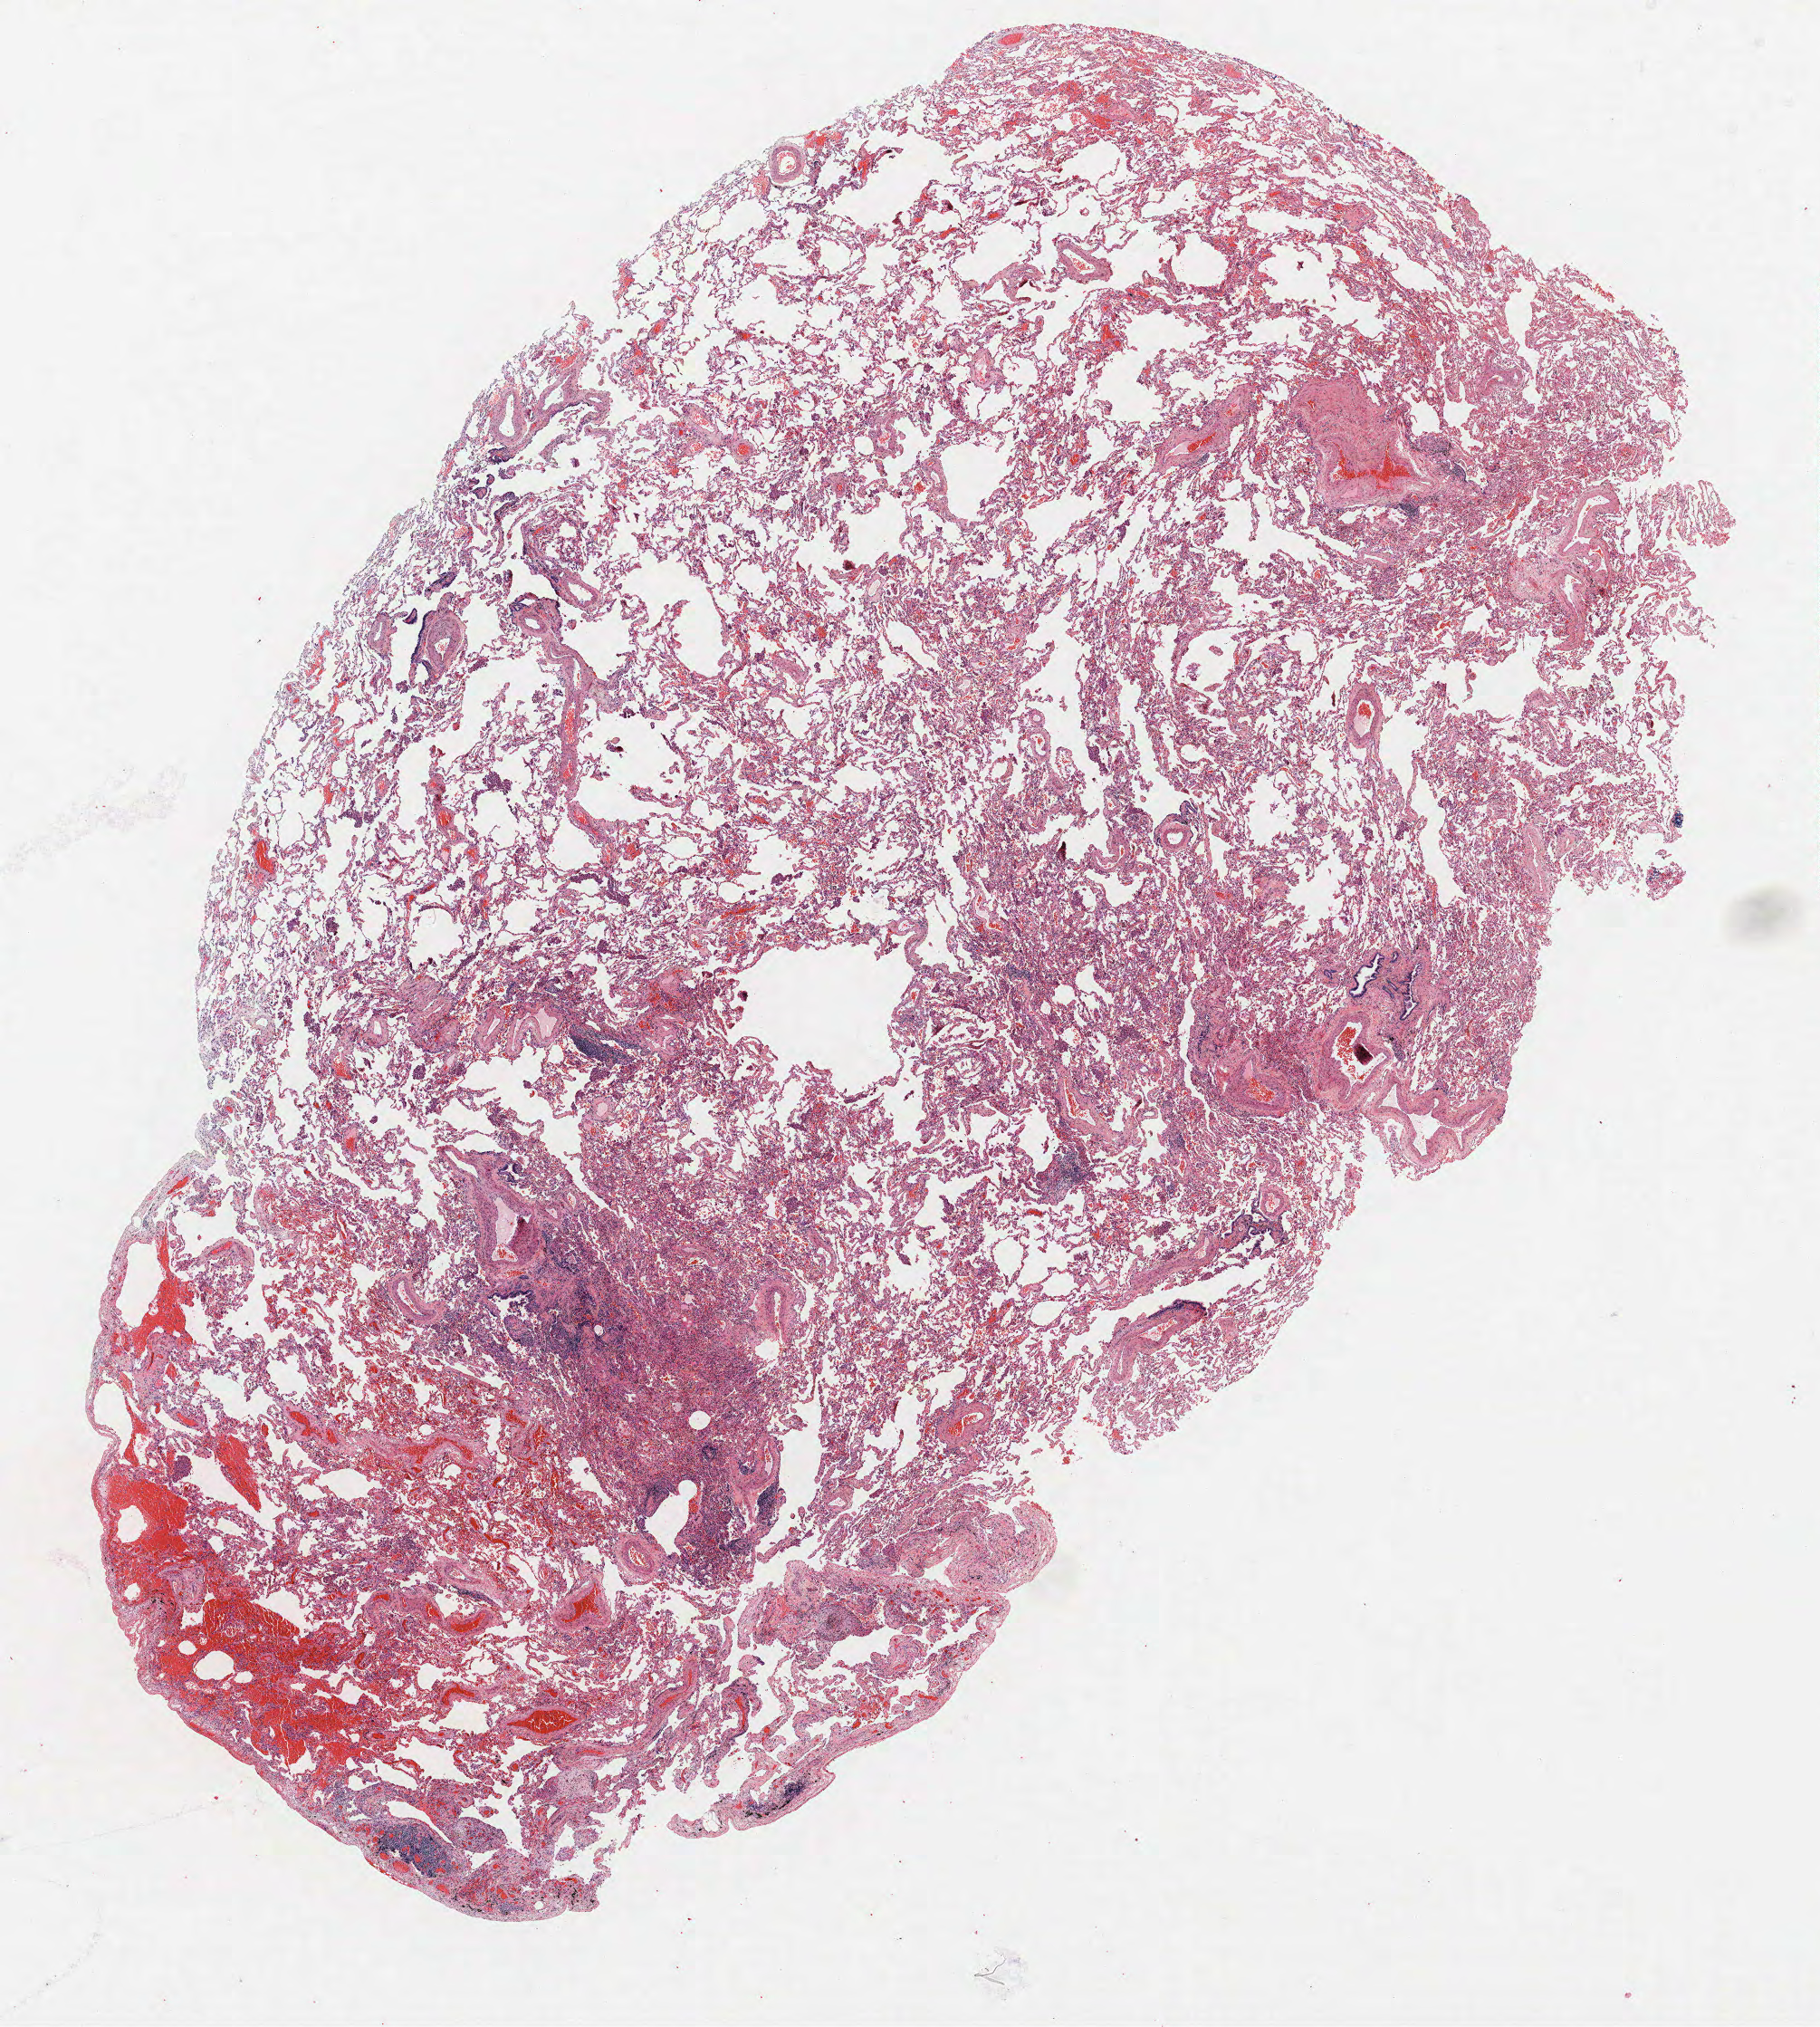
Whole-slide histology image, H&E — a low-resolution overview of the entire scanned area, about 16.1 x 17.9 mm (from a 40x scan); FFPE section; lung. Male patient, aged 59 at enrolment. Former smoker at enrolment. Grade: moderately differentiated (G2).
- tumour size (pathology): 15 mm
- participant's lung-cancer diagnosis: Squamous cell carcinoma, NOS (ICD-O-3 8070/3)
- primary tumour location (clinical record): right lower lobe
- stage (AJCC 6th edition): IA